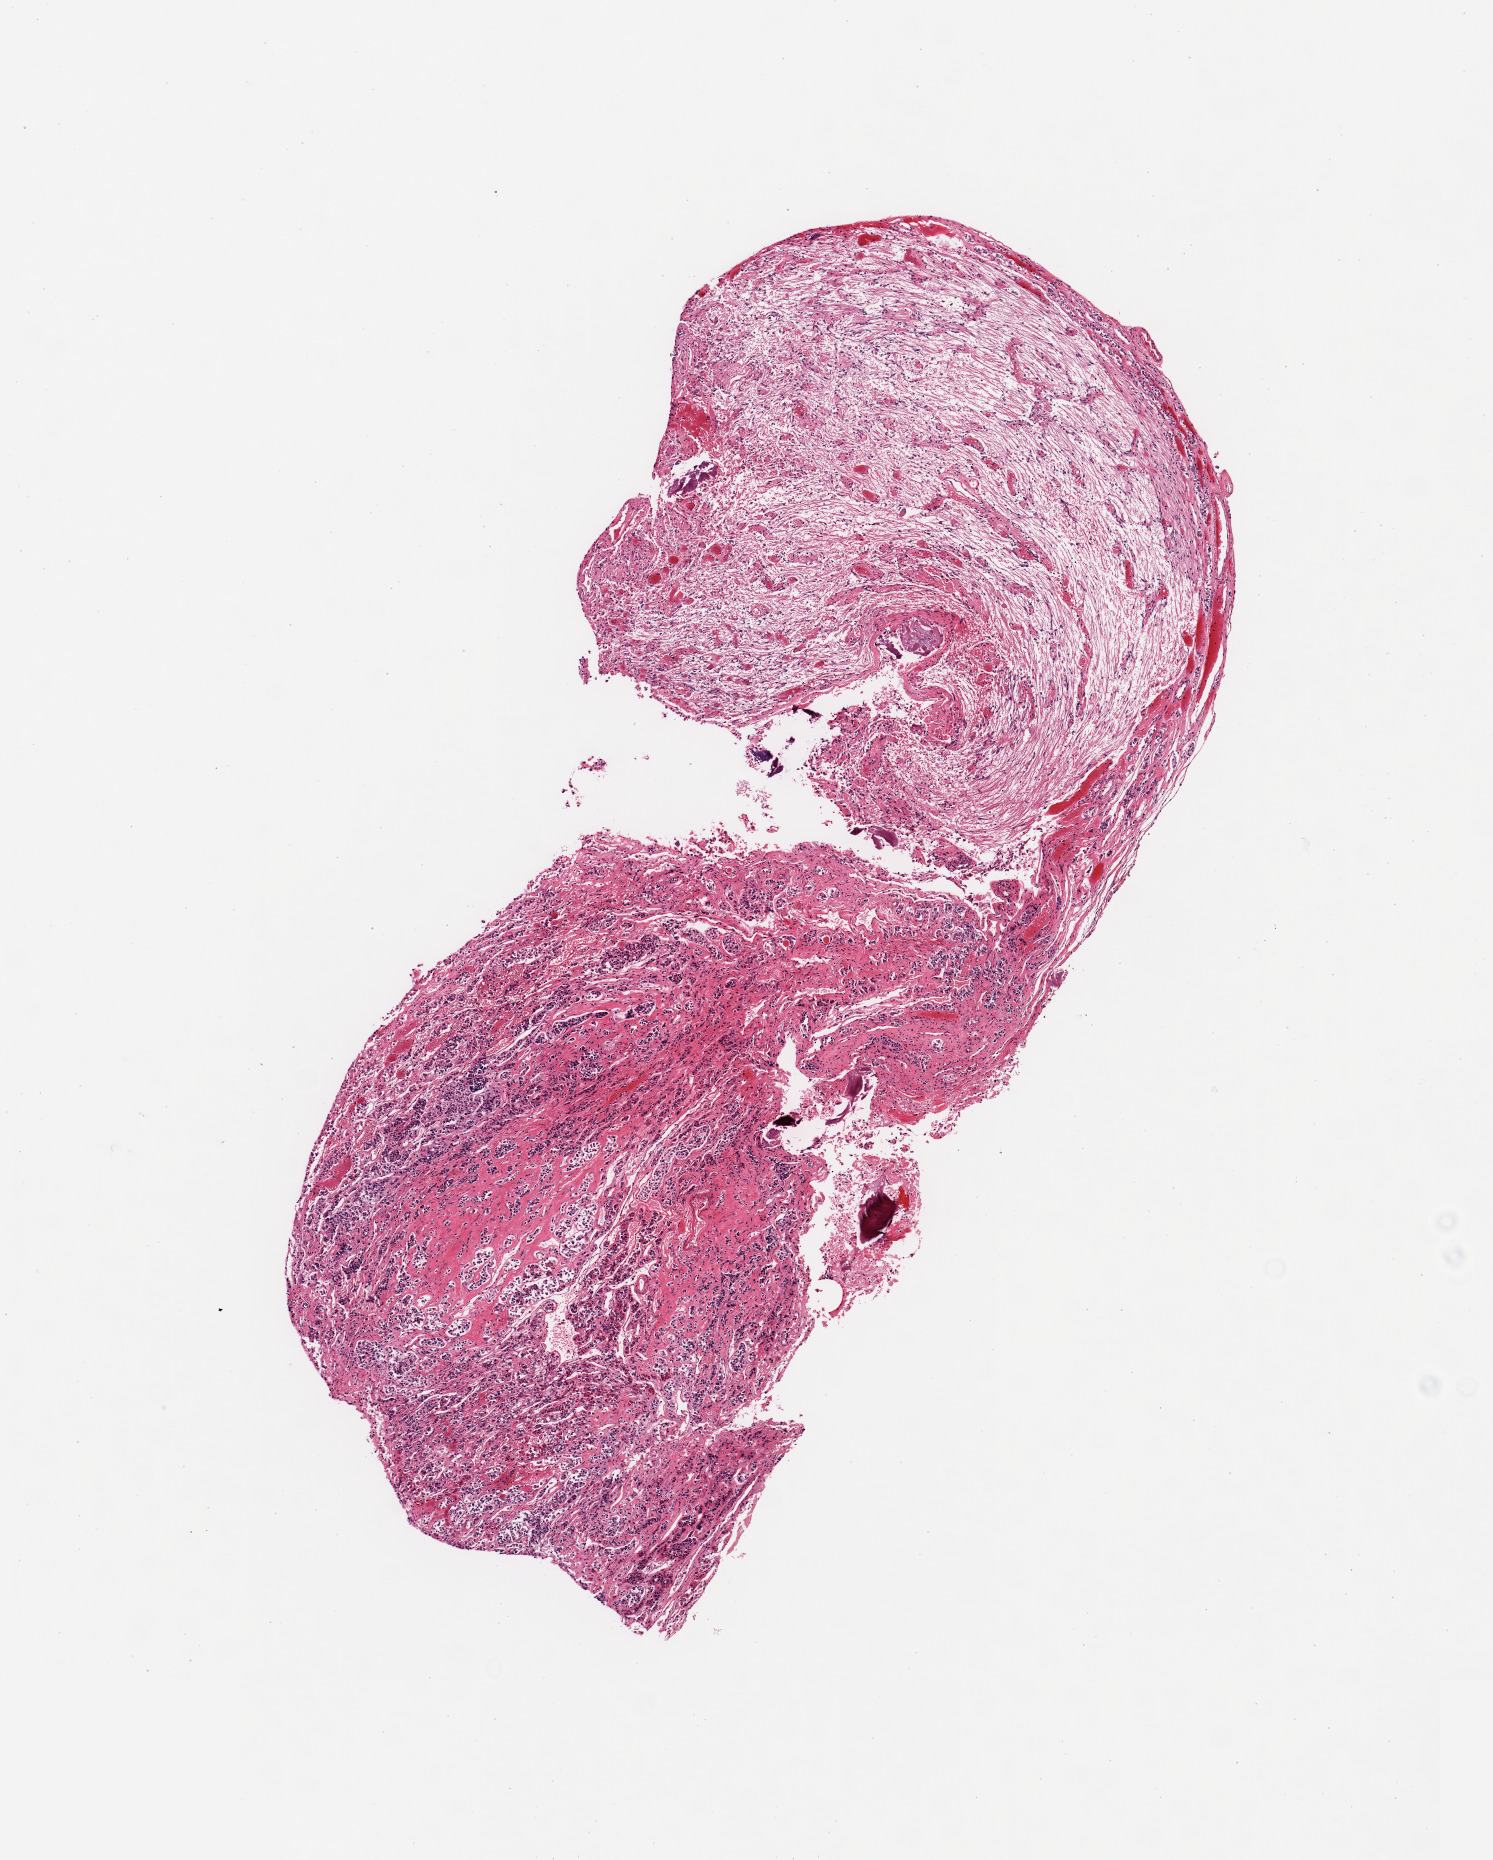
Digitized hematoxylin and eosin (H&E)-stained section, shown as a low-resolution overview of the whole scanned area (about 5.9 x 7.4 mm, from a 20x scan). PAXgene-fixed, paraffin-embedded tissue. Sampled site (target tissue): pituitary. Tissue donor sample. Donor sex: male.
Review note (as recorded): 1 piece; adenohypophysis and neurohypophysis.